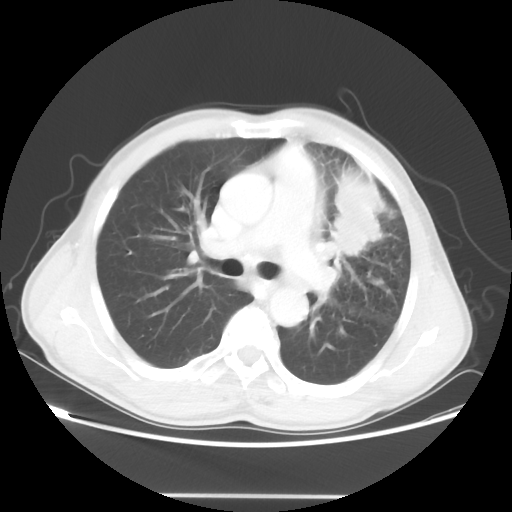
Chest CT, one axial slice. Position 32 of 55 along the scan axis. Reconstruction kernel STANDARD. 100 kVp. Lung window (W 1500 / L -600 HU). 5 mm slice thickness. 512 × 512 image matrix. Patient: male, 60 years. From the clinical record (not read from this slice): clinical TNM (as recorded): T3 N3 M0.
Outlined on this slice (rectangle marked by the reading radiologist):
- lung tumour (recorded histology: adenocarcinoma): bounding box (x1, y1, x2, y2) in pixels: (331, 169, 384, 258)